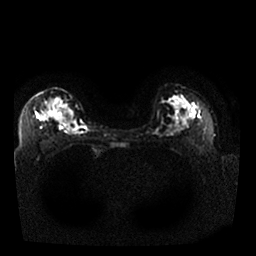
Breast MRI, one axial slice; slice 17 of 25 in the series (ordered by position); diffusion-weighted series; image 2 of 4 stored at this slice position (different b-values; order by instance number); 1.5 T; 4 mm slice thickness; 256 × 256 image matrix, field of view 340 × 340 mm. Female patient.
Structures marked on this image (manually delineated by an expert):
- tumour on diffusion-weighted imaging: bounding box (x1, y1, x2, y2) in pixels: (42, 105, 70, 123)